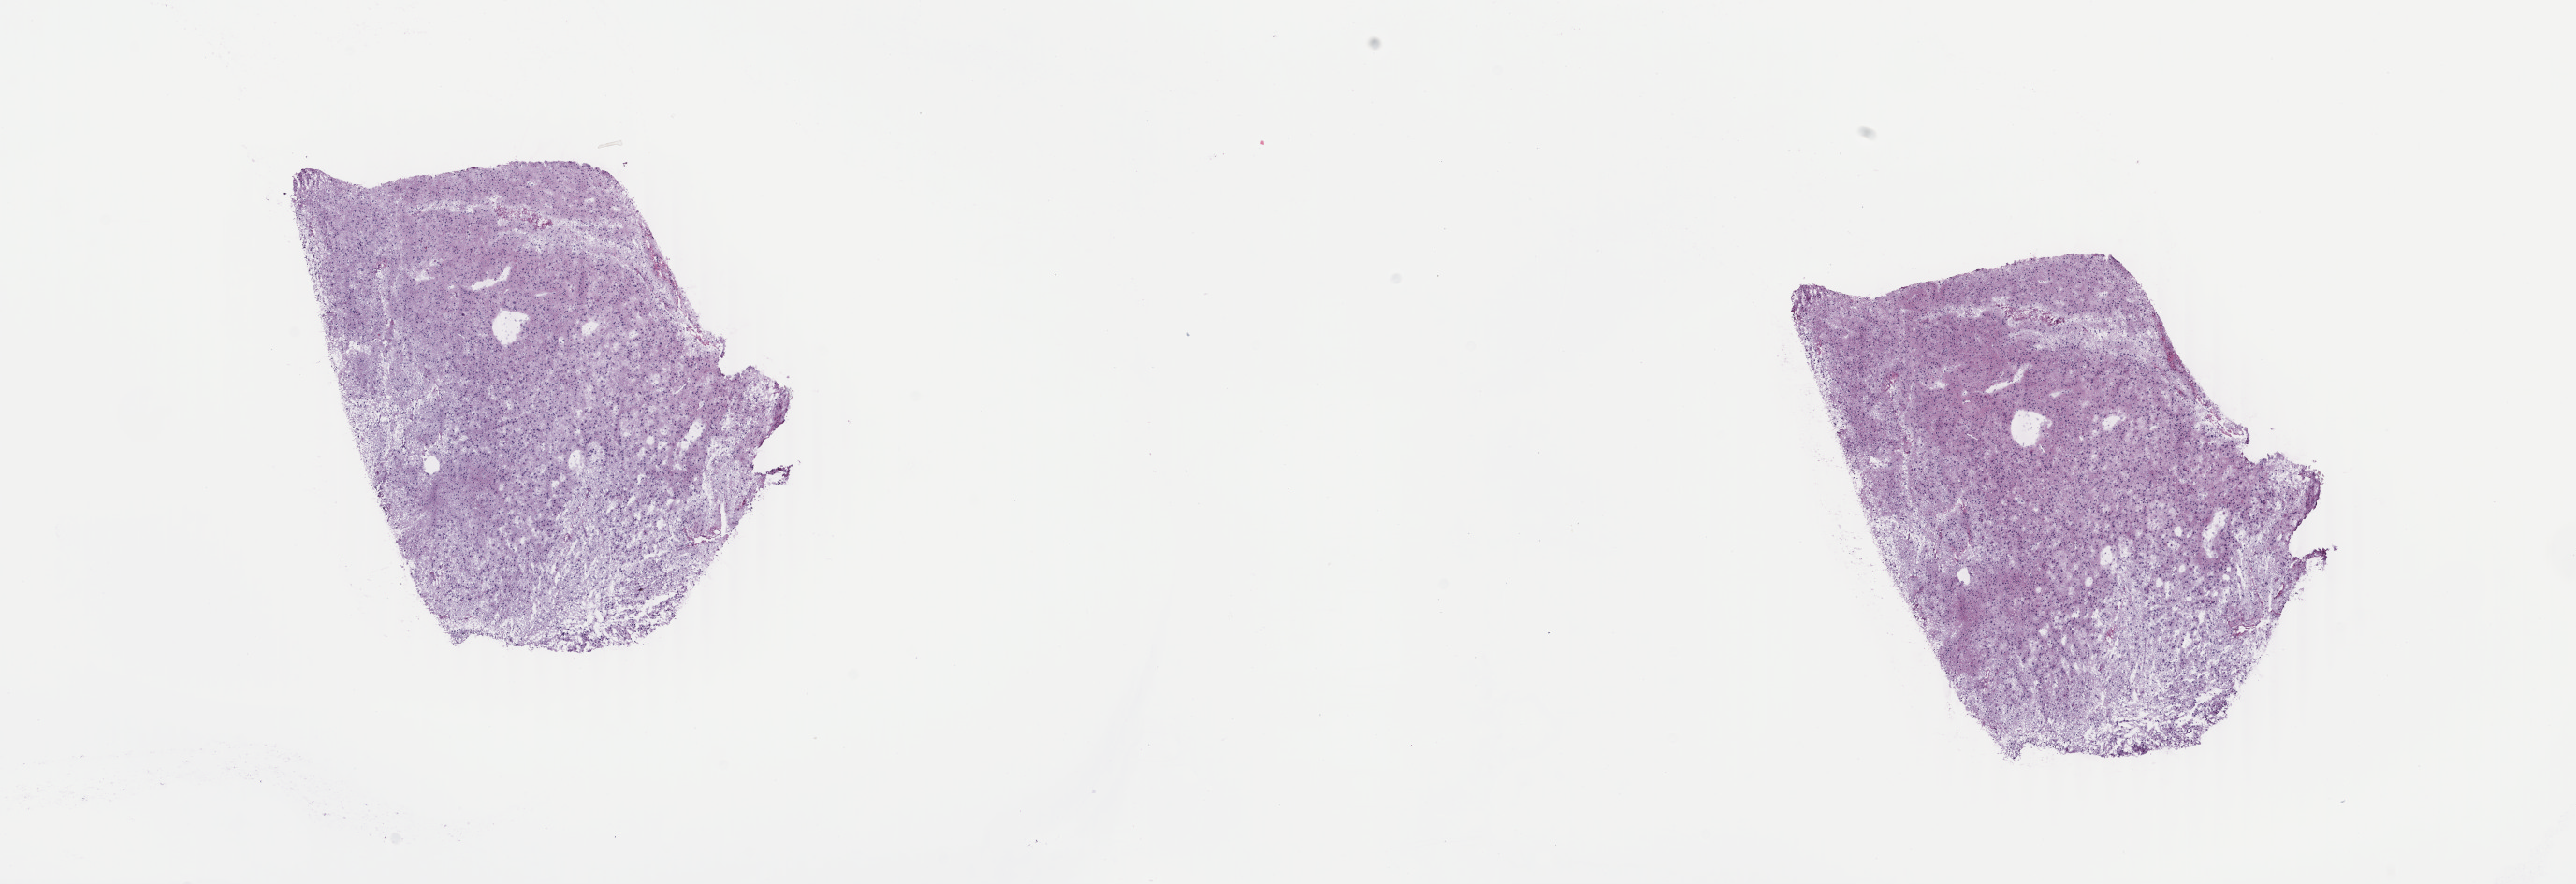
H&E whole-slide image — a low-resolution overview of the entire scanned area, about 21.9 x 7.5 mm (acquisition: 40x scan); frozen section from the top of the tissue portion; brain, primary tumour sample. Patient: female, age at initial diagnosis 50 years. Histologic grade: G2 (moderately differentiated). Pathologist review of this section (percent, as recorded): tumour cells 40%, tumour nuclei 85%, normal cells 10%, stromal cells 50%, necrosis 0%. Inflammatory infiltration, as recorded: lymphocyte infiltration 0%, monocyte infiltration 0%, neutrophil infiltration 0%.
Pathologic diagnosis: Oligodendroglioma, NOS (cerebrum). Laterality: right.